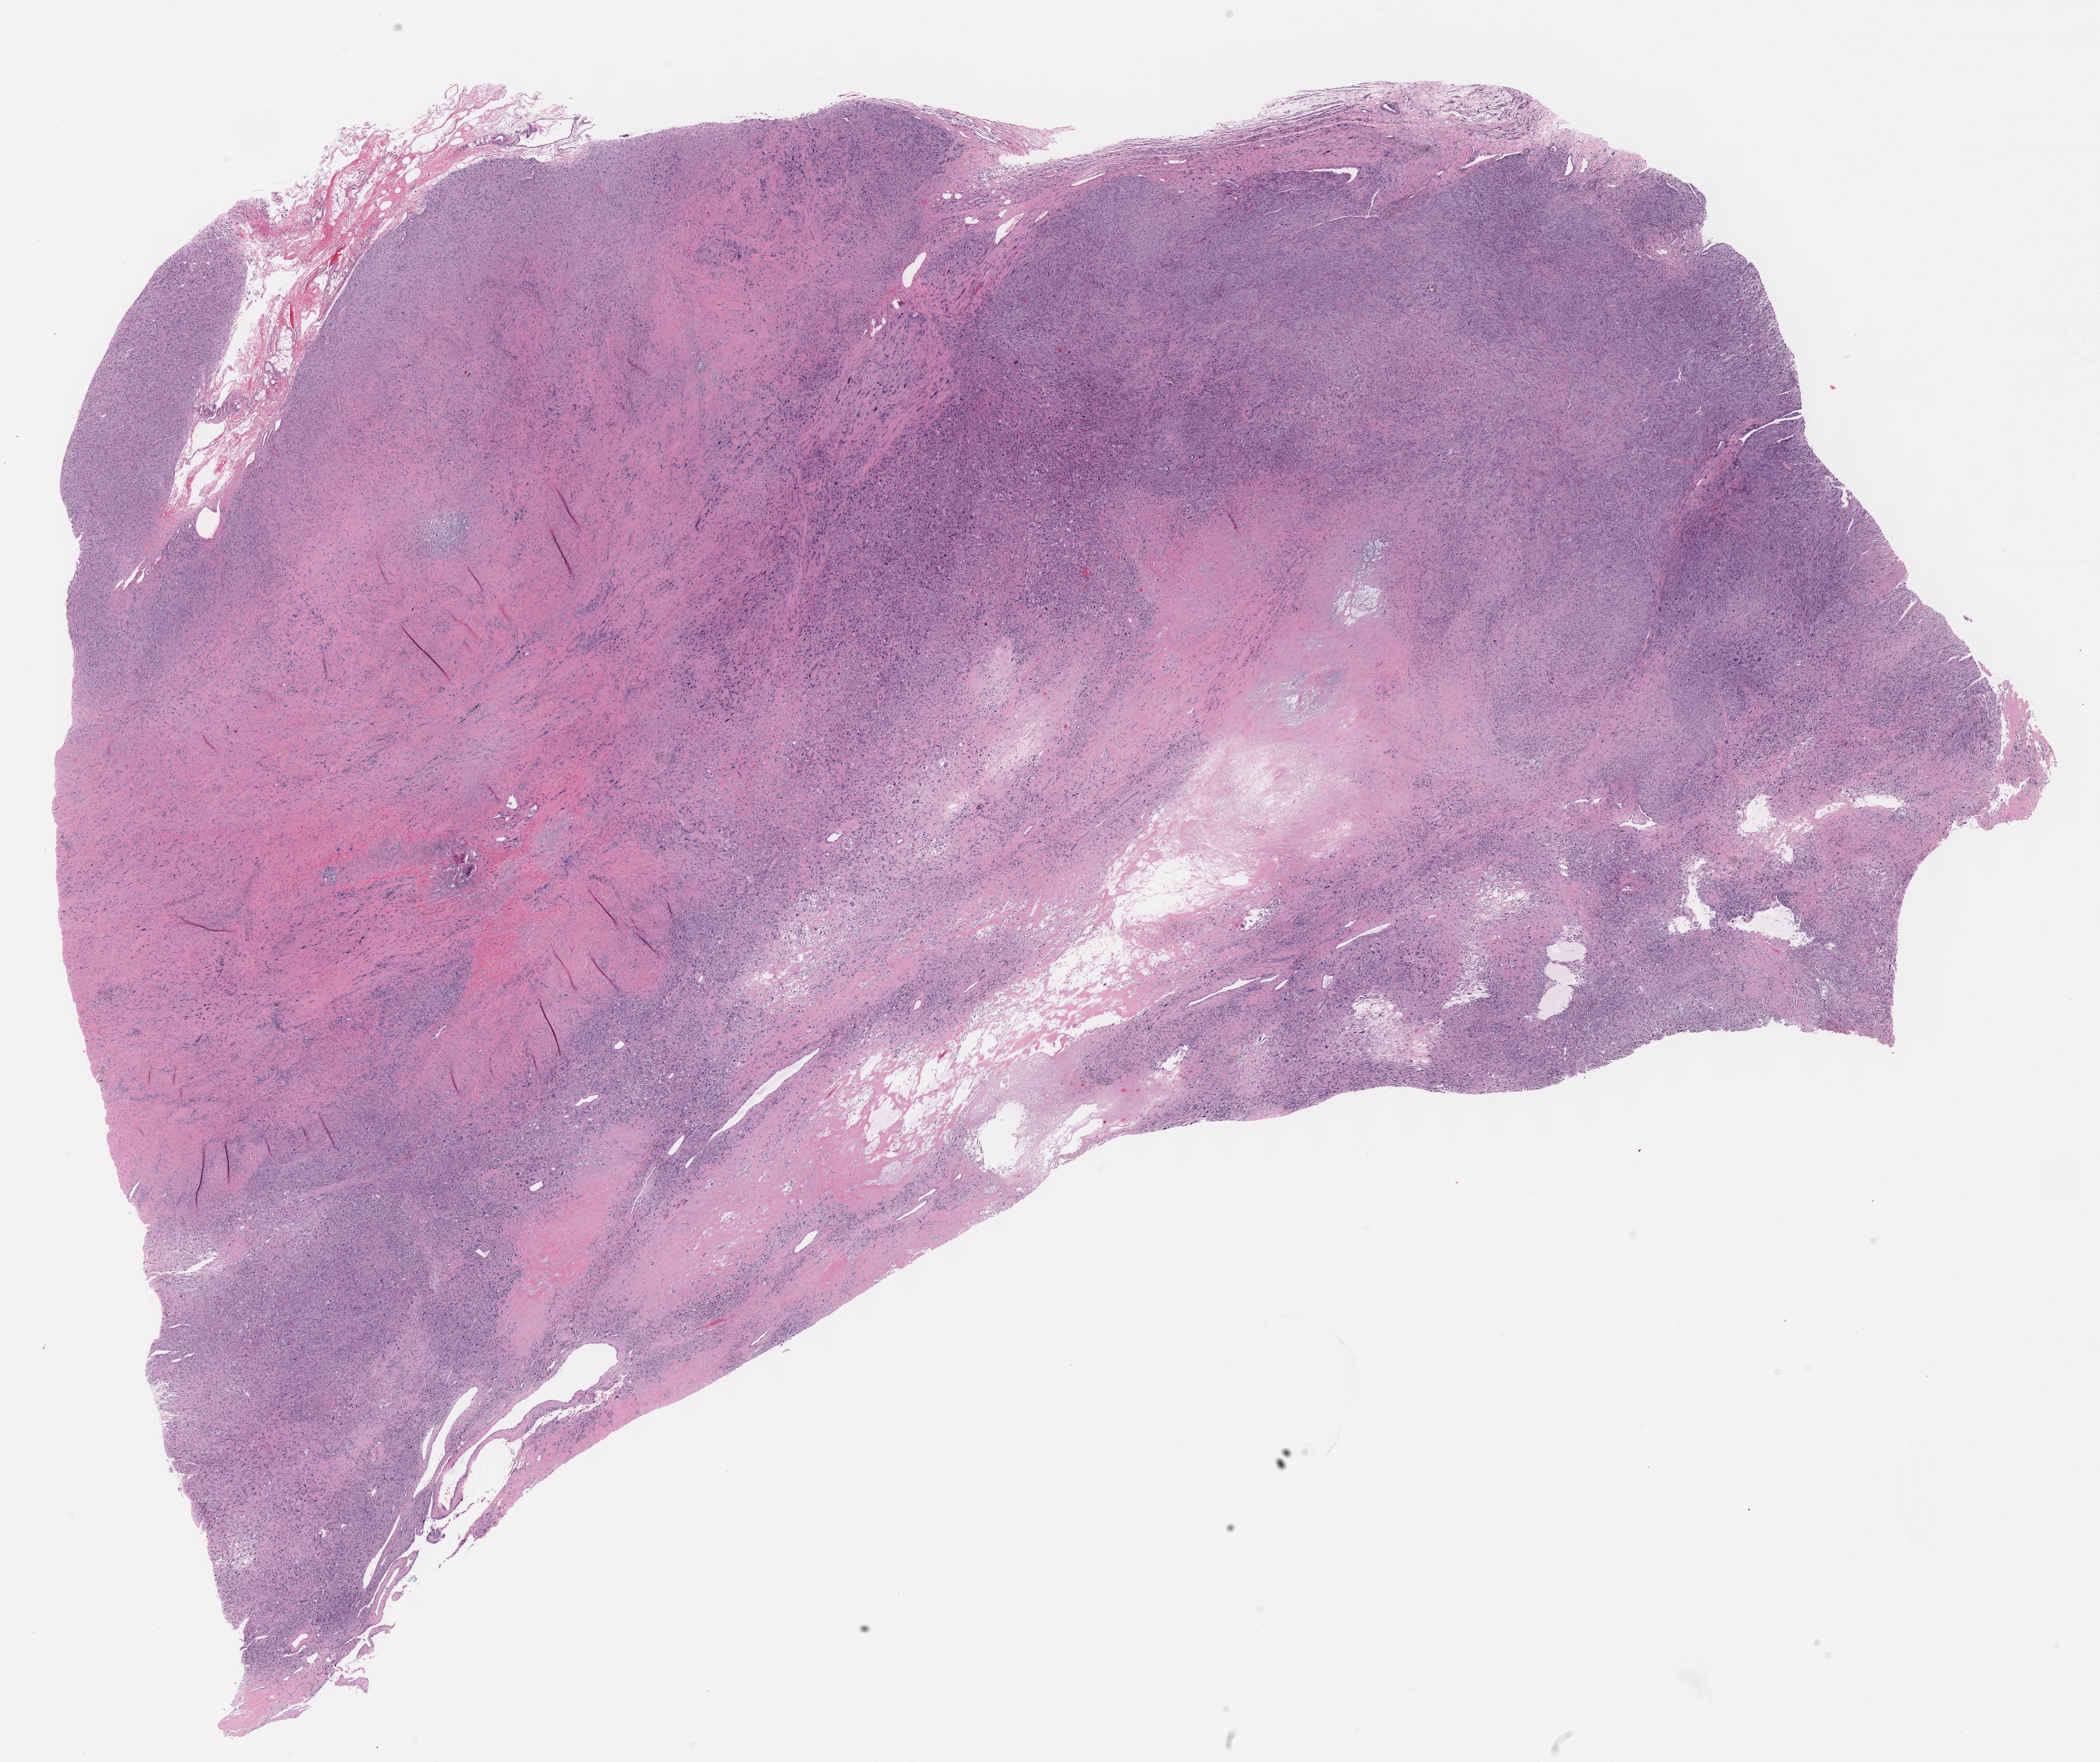
Hematoxylin and eosin (H&E) stained whole-slide image — a low-resolution overview of the entire scanned area, about 23.6 x 19.8 mm, formalin-fixed paraffin-embedded (FFPE) diagnostic section, sample: primary tumour, connective, subcutaneous and other soft tissues. Patient: male, age at initial diagnosis 76 years.
• pathologic diagnosis: Malignant fibrous histiocytoma (connective, subcutaneous and other soft tissues of thorax)